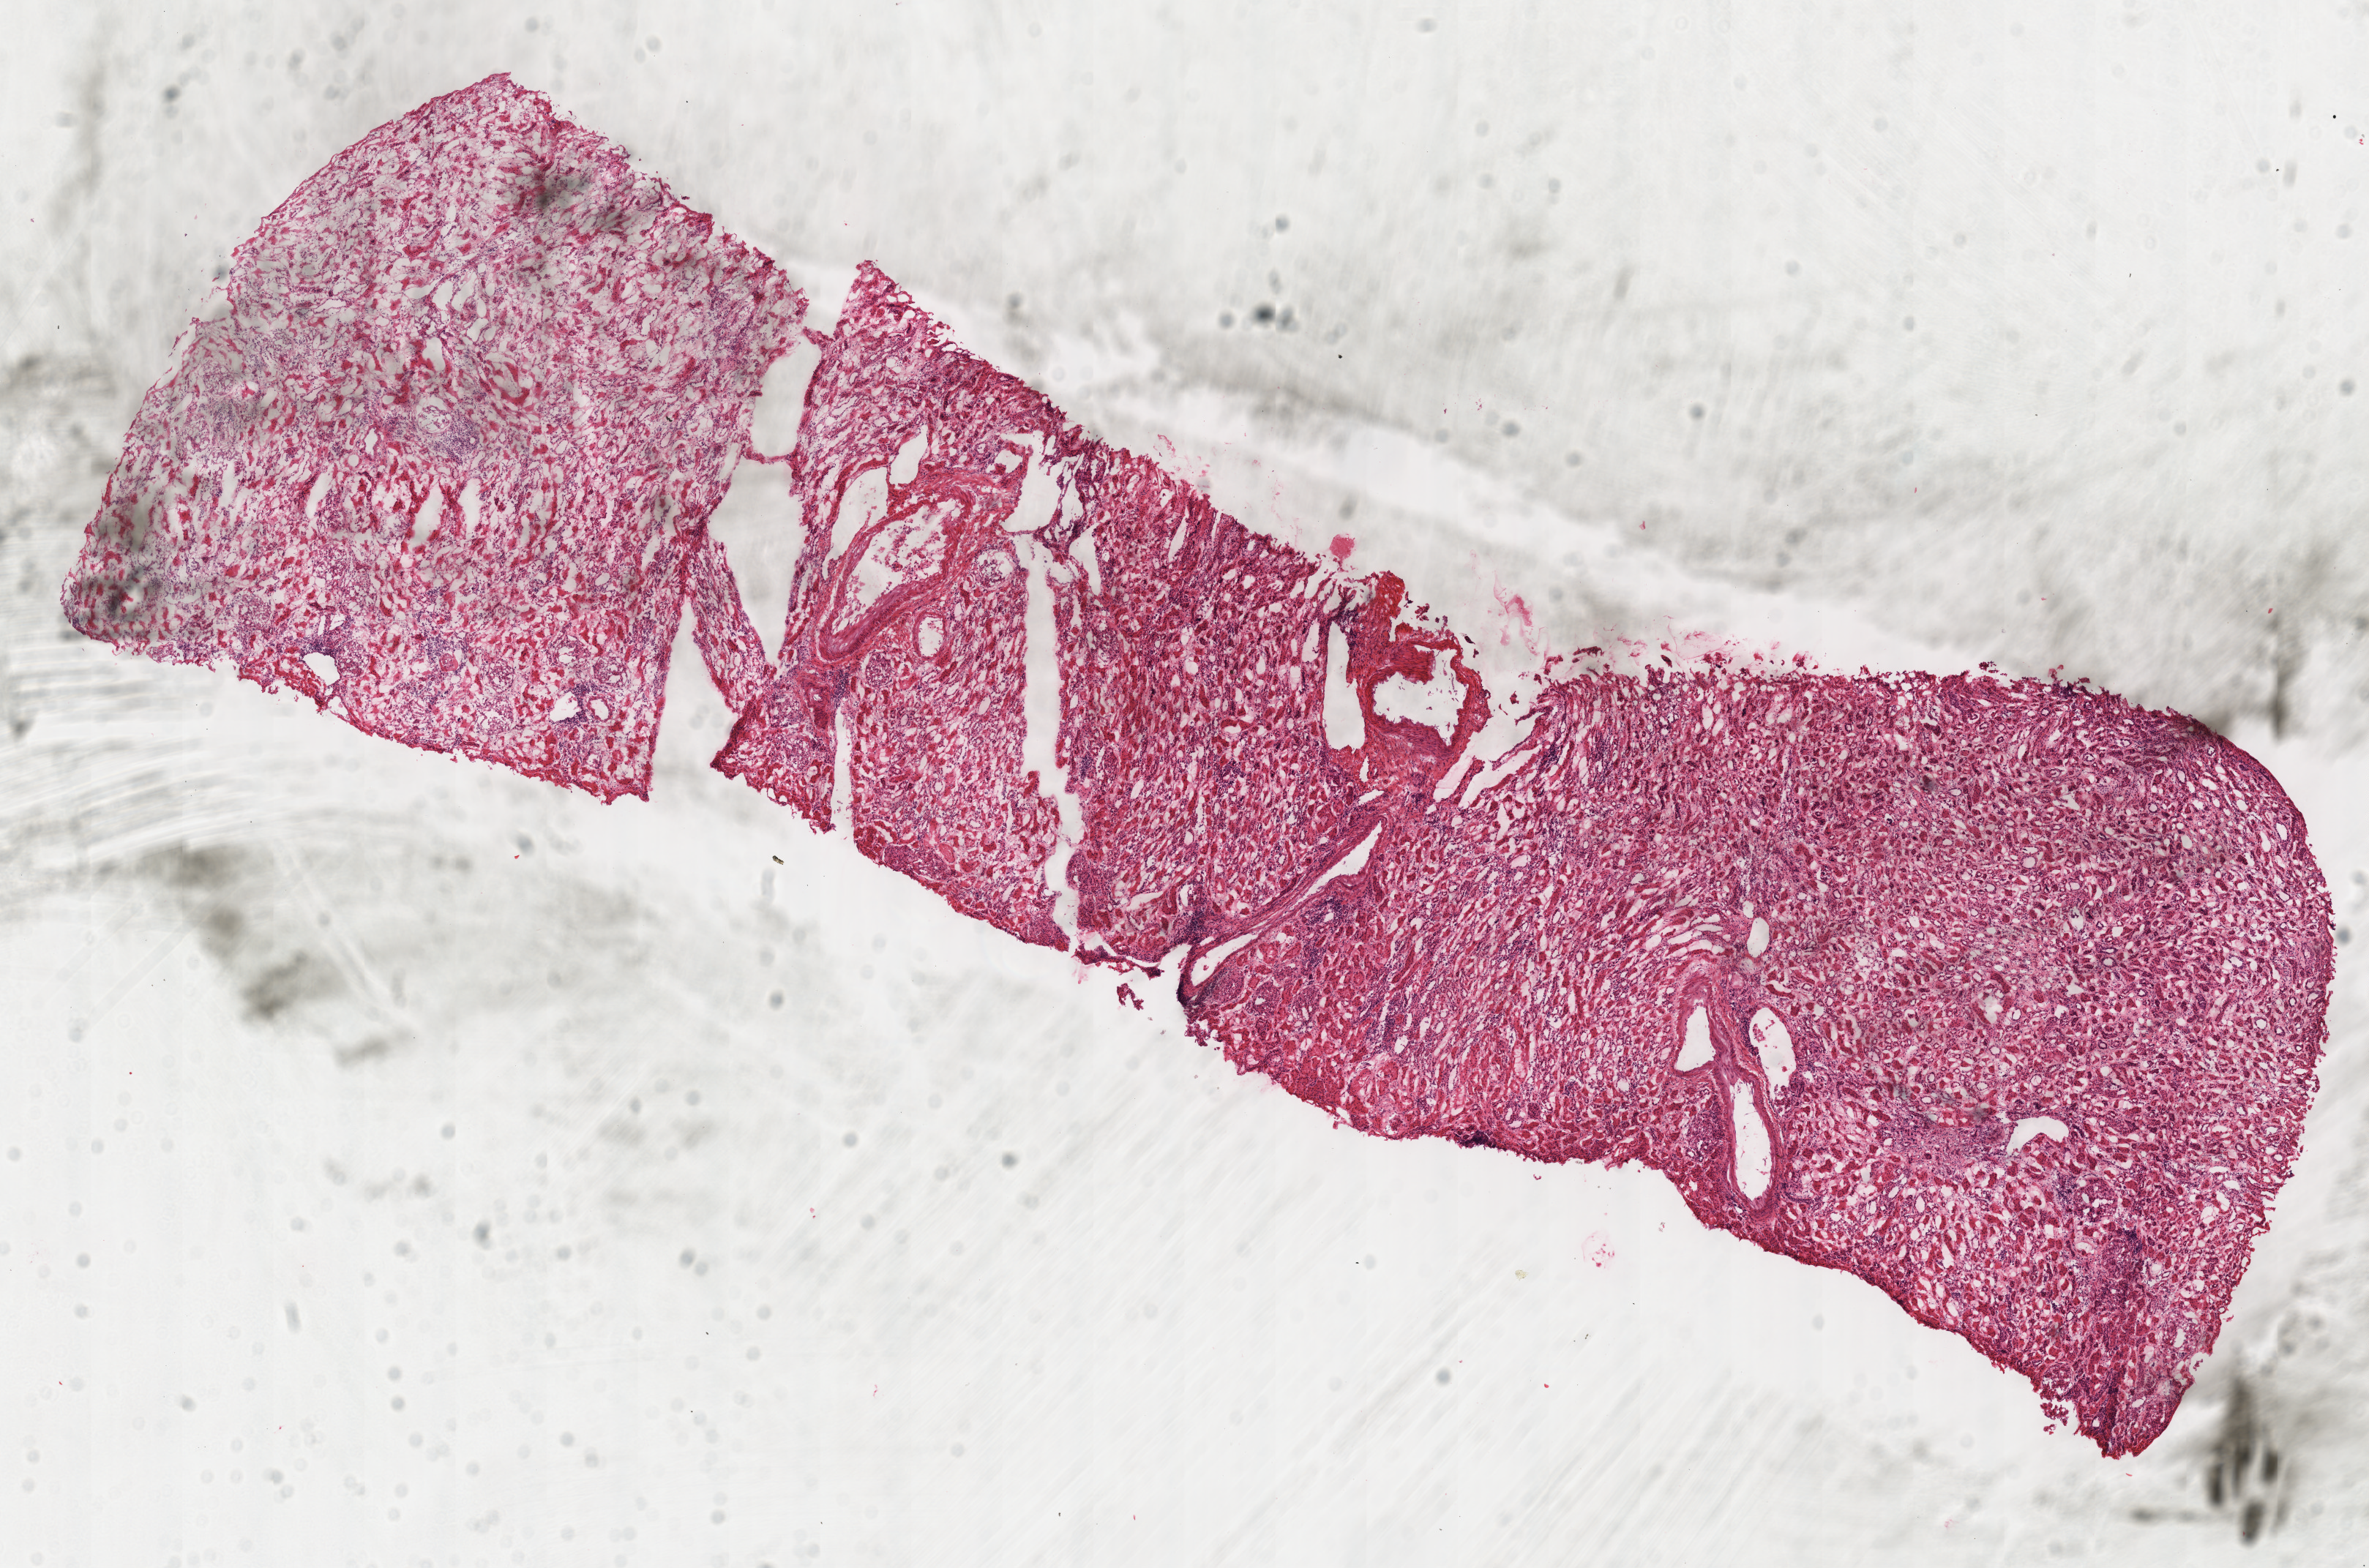
Hematoxylin and eosin (H&E) stained whole-slide image, shown as a low-resolution overview of the whole scanned area (about 12.7 x 8.4 mm, slide scanned at 40x). Frozen section. Kidney, solid tissue normal (non-tumour tissue) sample. Patient: female, age at initial diagnosis 47 years. Infiltration values recorded for this section: lymphocyte infiltration 7%, monocyte infiltration 0%, neutrophil infiltration 0%.
This section: solid tissue normal (non-tumour) sample from the same patient. Patient diagnosis: Renal cell carcinoma, chromophobe type.